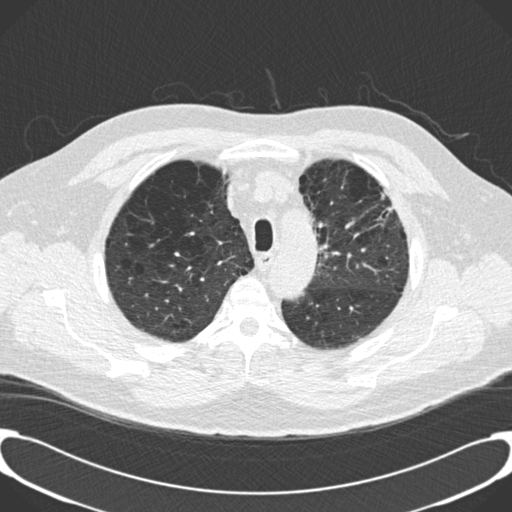
Low-dose screening chest CT, one axial slice. Position 158 of 189 along the scan axis. Reconstruction kernel B30f. Lung window (W 1500 / L -600 HU). 2 mm slice thickness. 512 × 512 image matrix.
Annotated regions visible in this slice (manually delineated by an expert):
- lesion 1 (tumor, upper lobe of left lung): bounding box <380,192,393,218> (left, top, right, bottom; pixels)